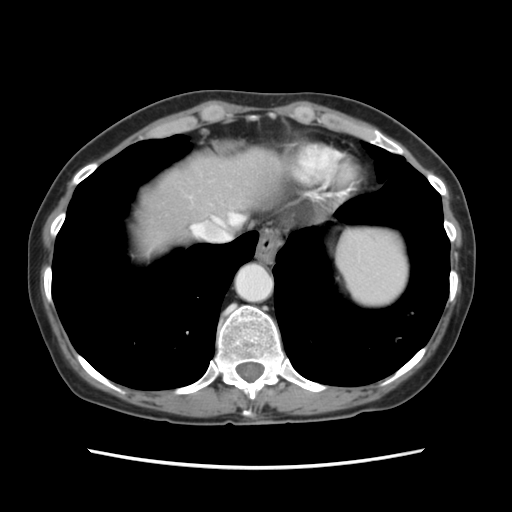
Contrast-enhanced abdominal CT, one axial slice. Soft-tissue window (W 400 / L 40 HU). 2.5 mm slice thickness. 512 × 512 image matrix. Female patient, age 70 years. Case-level facts recorded for this patient, not image findings: diagnosis: colorectal cancer liver metastases, imaged before liver resection; multiple liver metastases: no.
Annotated regions visible in this slice (expert manual segmentation):
- hepatic veins: bounding box <195,222,232,242> (left, top, right, bottom; pixels)
- liver: <131,151,282,257>
- planned liver remnant (the part of the liver to remain after resection): <157,151,282,228>